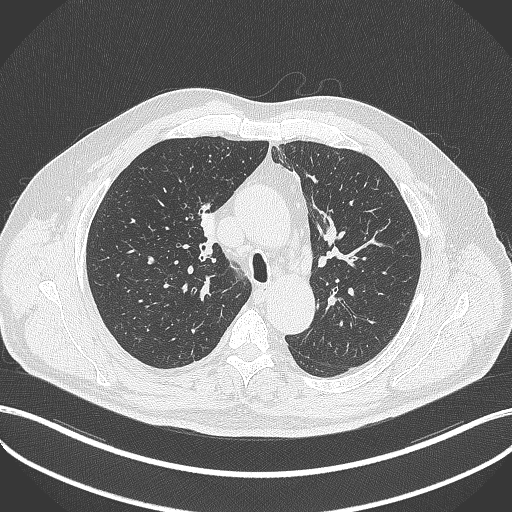
Chest CT, one axial slice. Slice 264 of 411 in the series (ordered by position). Reconstruction kernel B70f. 120 kVp. Lung window (W 1500 / L -600 HU). 1 mm slice thickness. 512 × 512 image matrix, field of view 400 × 400 mm. Male patient, age 60 years. From the clinical record (not read from this slice): clinical TNM (as recorded): T1b N1 M0.
Structures marked on this image (rectangle marked by the reading radiologist):
- lung tumour (recorded histology: squamous cell carcinoma): bounding box (x1, y1, x2, y2) in pixels: (197, 212, 226, 250)